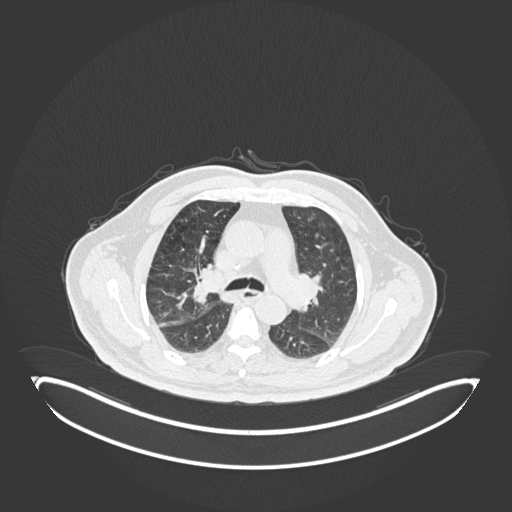
Chest CT, one axial slice; position 117 of 247 along the scan axis; reconstruction kernel B30f; lung window (W 1500 / L -600 HU); 1 mm slice thickness; 512 × 512 image matrix. Patient: male, 72 years. Case-level facts recorded for this patient, not image findings: clinical TNM (as recorded): T1c N0 M0.
Annotated regions visible in this slice (bounding box drawn by a radiologist):
- lung tumour (recorded histology: squamous cell carcinoma): box from (x=187, y=261) to (x=212, y=307) px